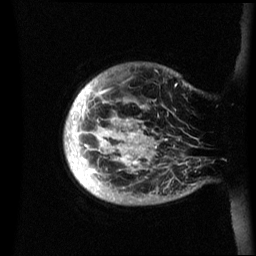
Breast MRI (dynamic contrast-enhanced), one sagittal slice; slice 5 of 60 in the series (ordered by position); dynamic contrast-enhanced series, image 2 of 3 at this slice position (ordered by acquisition); 1.5 T; TE 4.2 ms, TR 8.4 ms; 256 × 256 image matrix, field of view 230 × 230 mm. Patient: female, 48 years.
Structures marked on this image (semi-automatic segmentation, software-assisted and operator-edited):
- analysis volume of interest (the breast-tissue region the enhancement analysis was run in; not a lesion): box from (x=64, y=63) to (x=202, y=205) px
- tumour enhancement mask (voxels above the 70 % enhancement threshold inside the analysis volume of interest): (x=66, y=88)–(x=158, y=175)